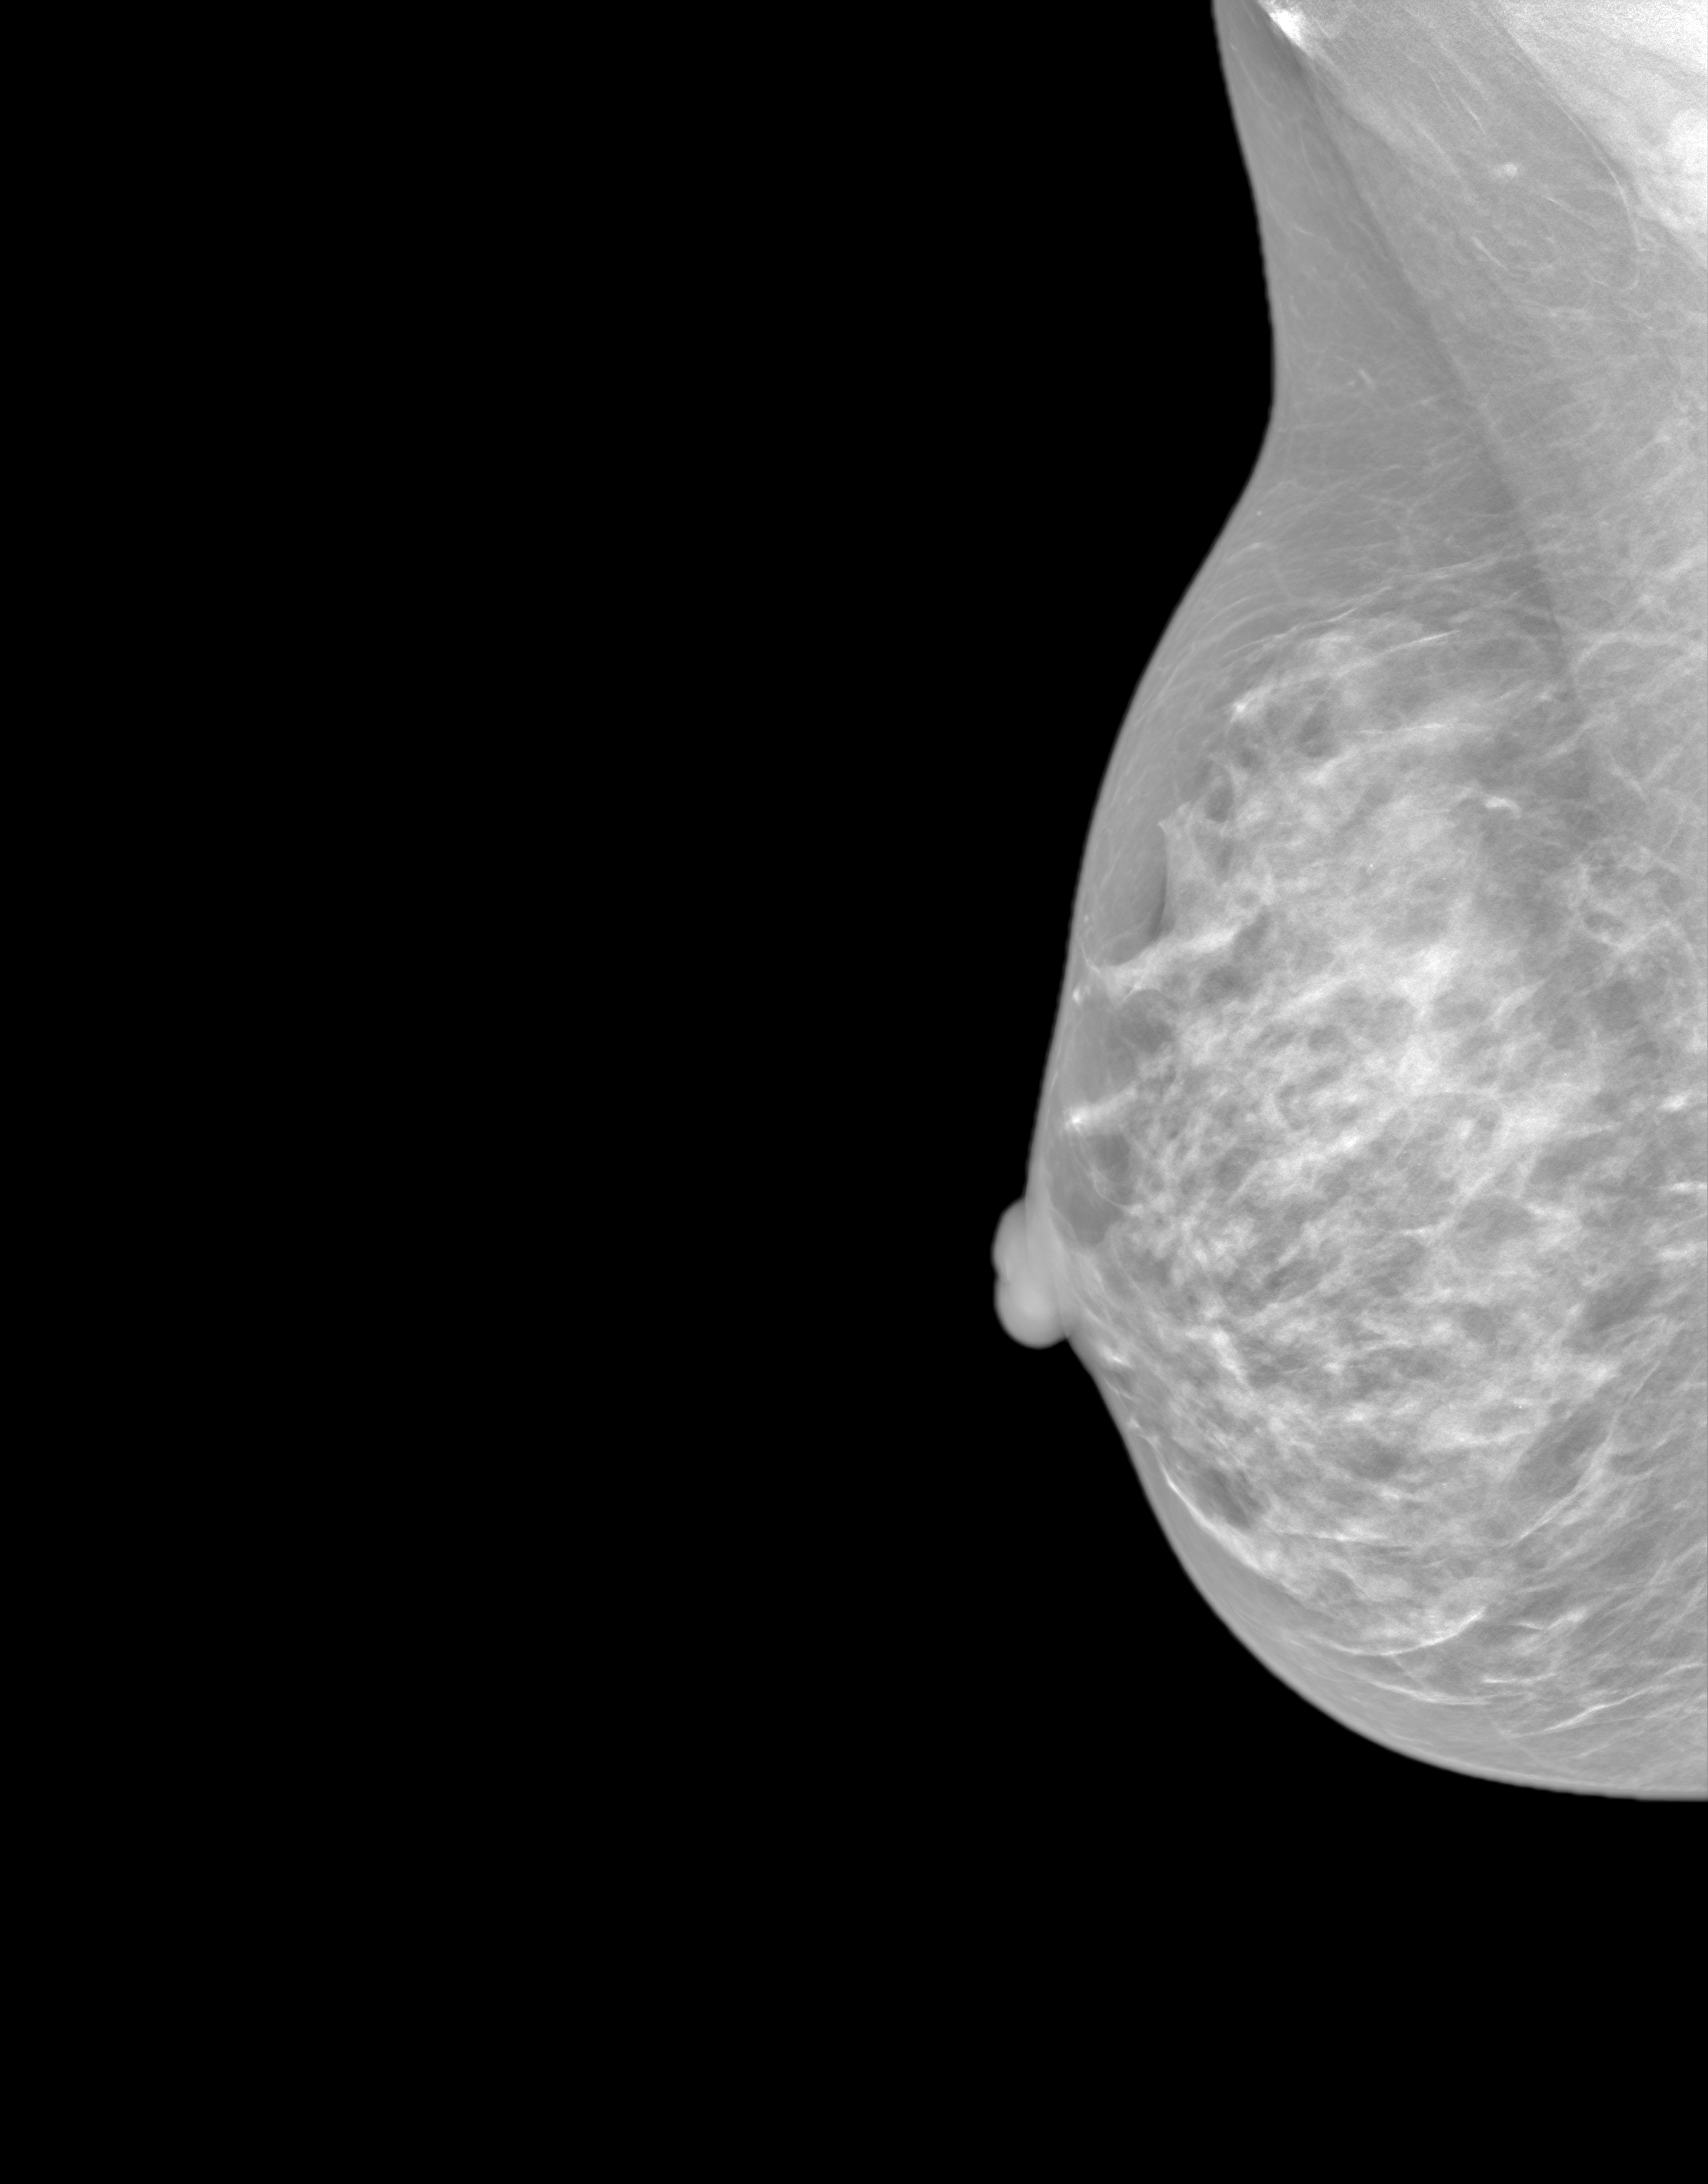
Annual screening mammography examination. Female patient, age 43 years.
Image type: synthesized 2-D view from tomosynthesis. Breast: right. Projection: MLO view.